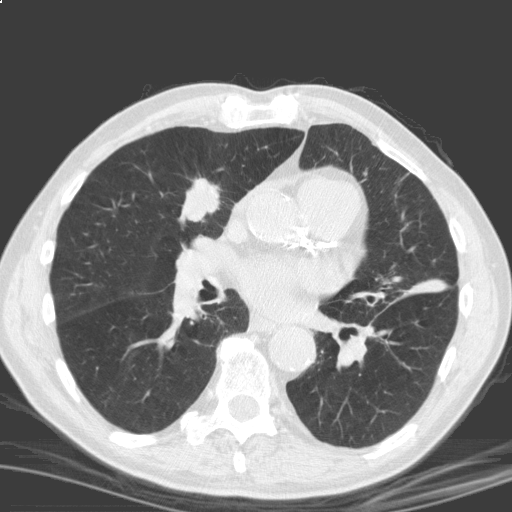
Chest CT (low-dose screening protocol), one axial image, second screening round (one year after baseline), lung window (W 1500 / L -600 HU), 3.2 mm slice thickness, standard (soft-tissue) reconstruction kernel (C), 512 × 512 image matrix. Male participant, aged 69 years at enrolment. Current smoker at enrolment.
Lesion marked by an expert reader, box from (x=170, y=166) to (x=232, y=226) px. The screening reader recorded 2 non-calcified nodules or masses ≥4 mm on this exam (right upper lobe, left lower lobe); which of them this box marks is not recorded. Official screen result: positive, other.